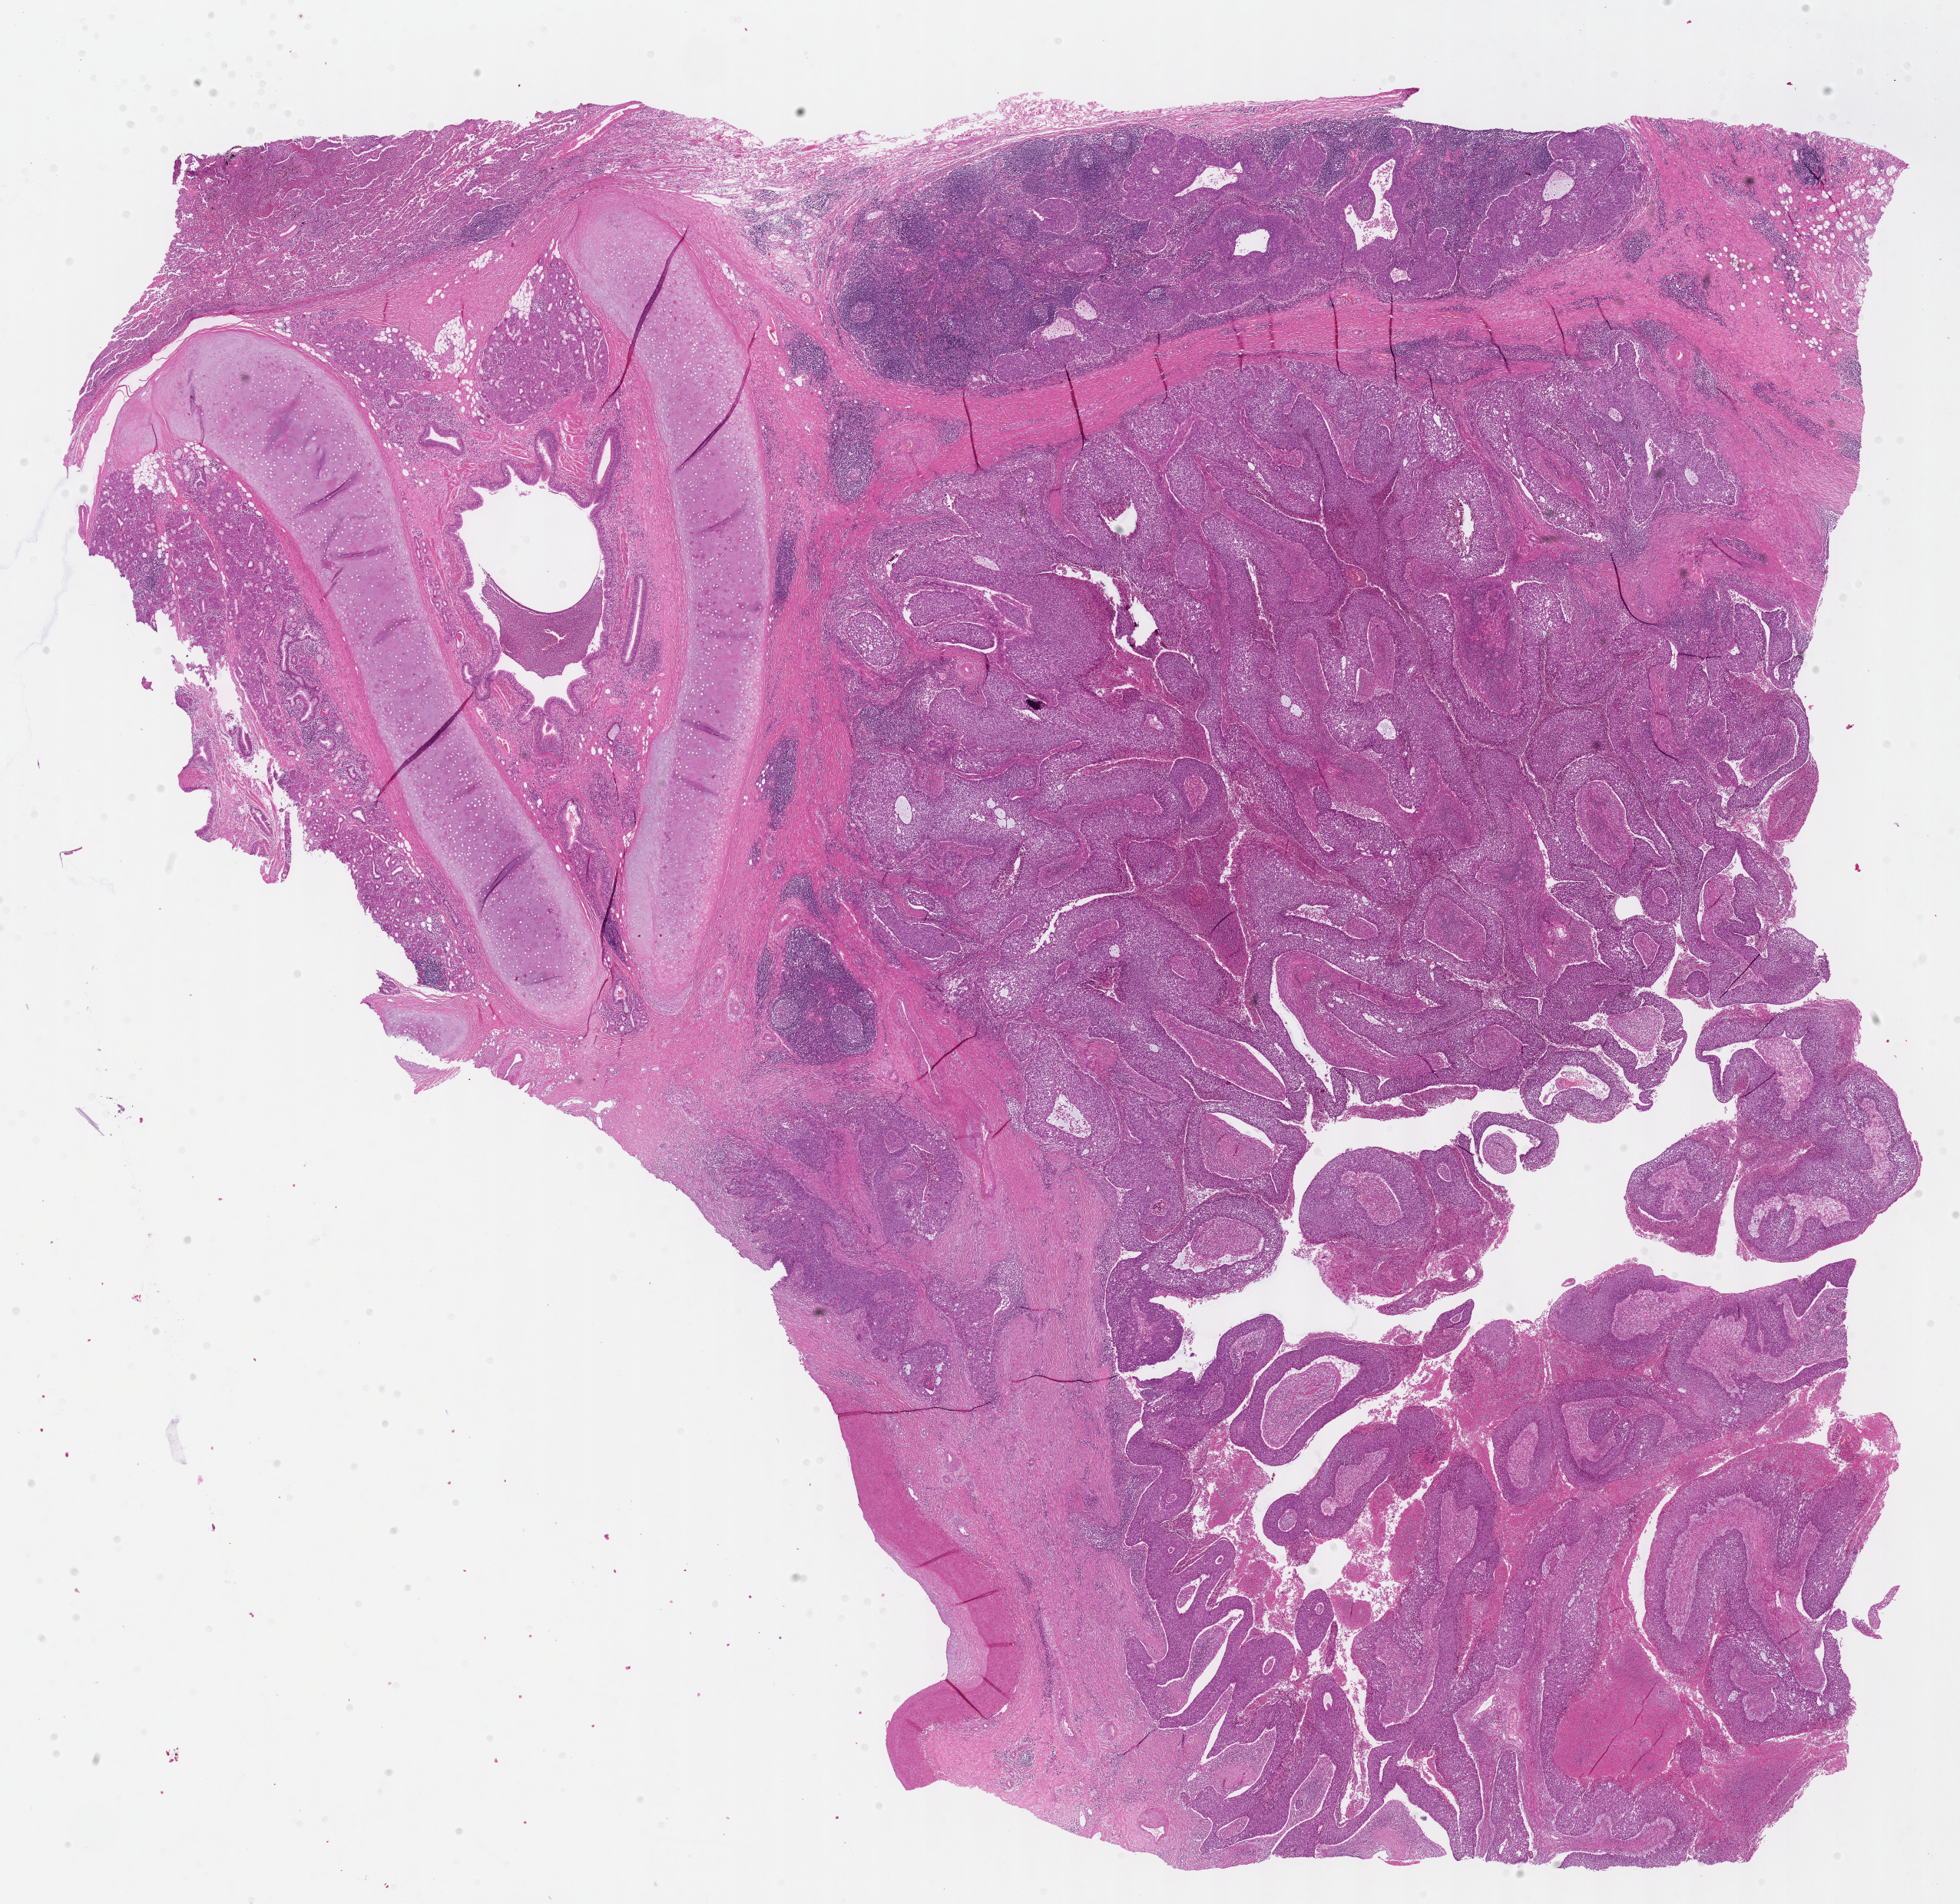
Whole-slide histology image, H&E, low-resolution overview of the scanned area, about 20.6 x 20.0 mm (slide scanned at 40x), formalin-fixed paraffin-embedded (FFPE) diagnostic section, sample: primary tumour, lung. Male, age 59 years at initial diagnosis.
- AJCC pathologic stage: IIIA (6th edition)
- histologic diagnosis: Basaloid squamous cell carcinoma